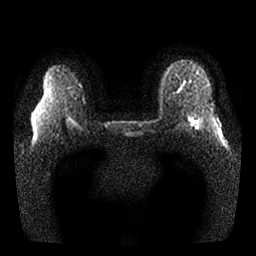
Breast MRI, one axial slice; slice 21 of 25 in the series (ordered by position); diffusion-weighted series; image 2 of 4 stored at this slice position (different b-values; order by instance number); 1.5 T; 4 mm slice thickness; 256 × 256 image matrix, field of view 340 × 340 mm. Female patient.
Outlined on this slice (expert manual segmentation):
- tumour on diffusion-weighted imaging: box from (x=193, y=119) to (x=198, y=125) px